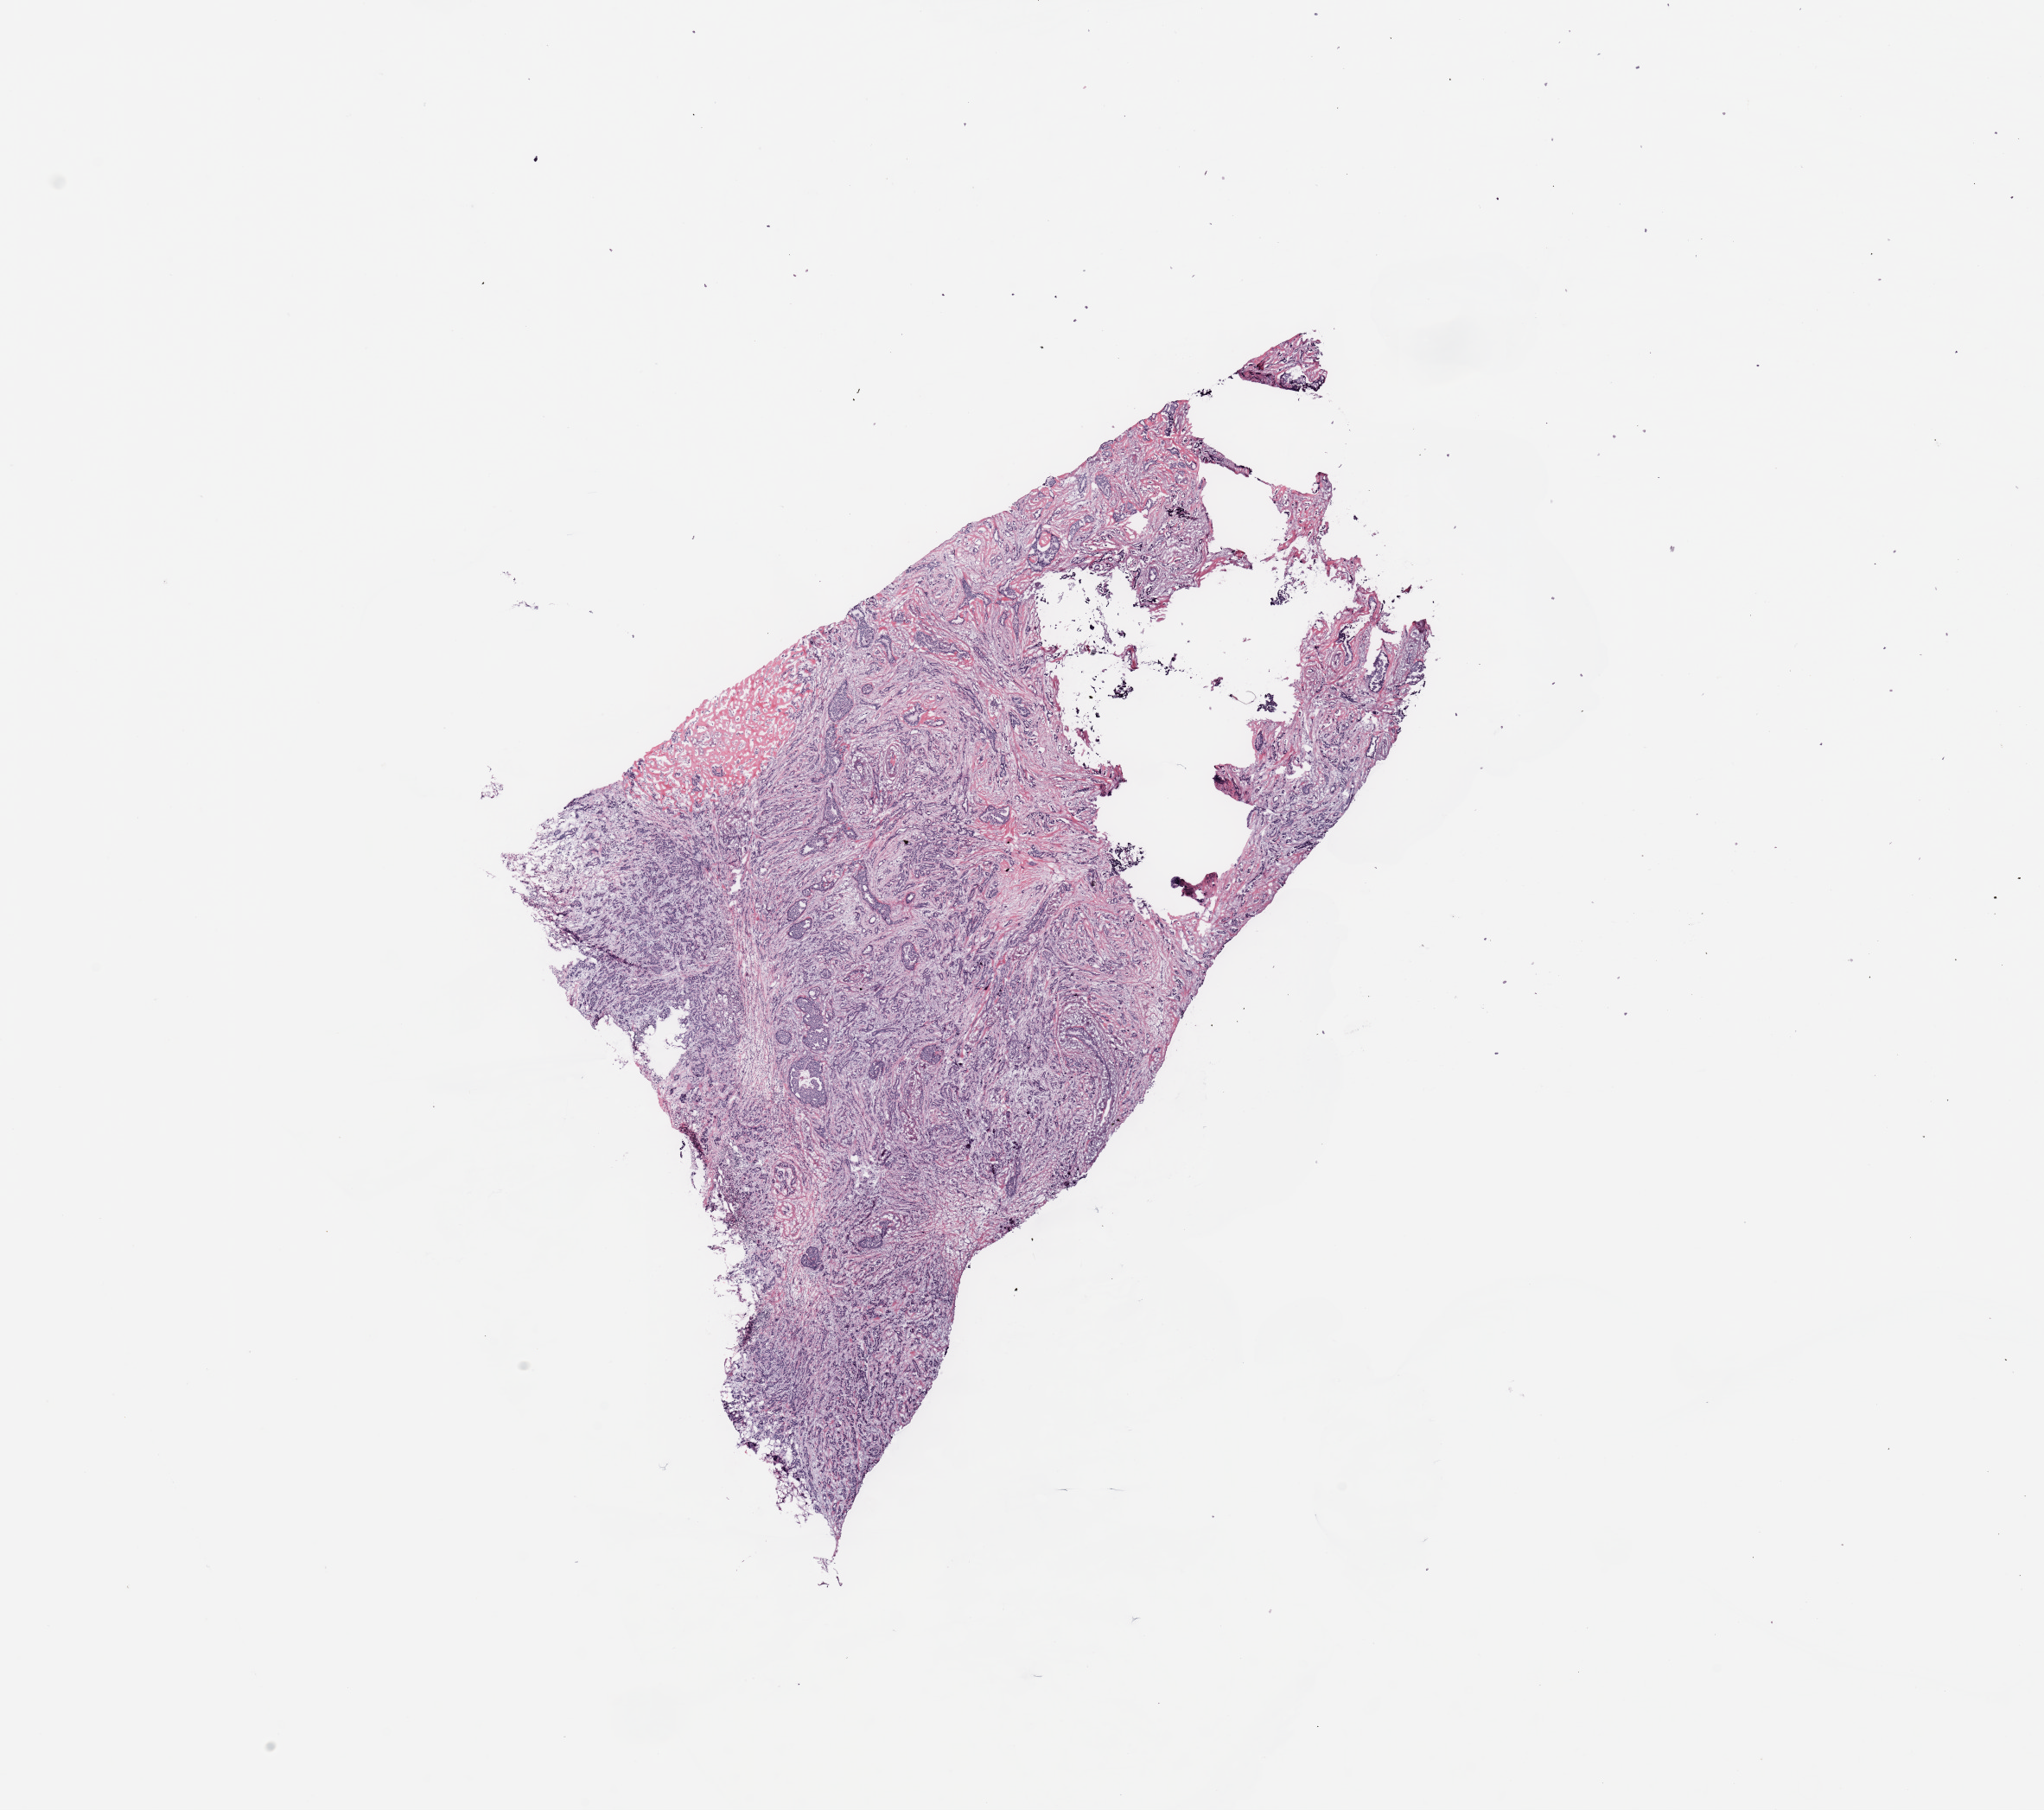
Hematoxylin and eosin (H&E) stained whole-slide image, a low-resolution overview of the entire scanned area, about 18.7 x 16.6 mm (from a 20x scan); breast, tissue type not recorded.
Patient diagnosis (cohort enrolment): breast cancer (breast).